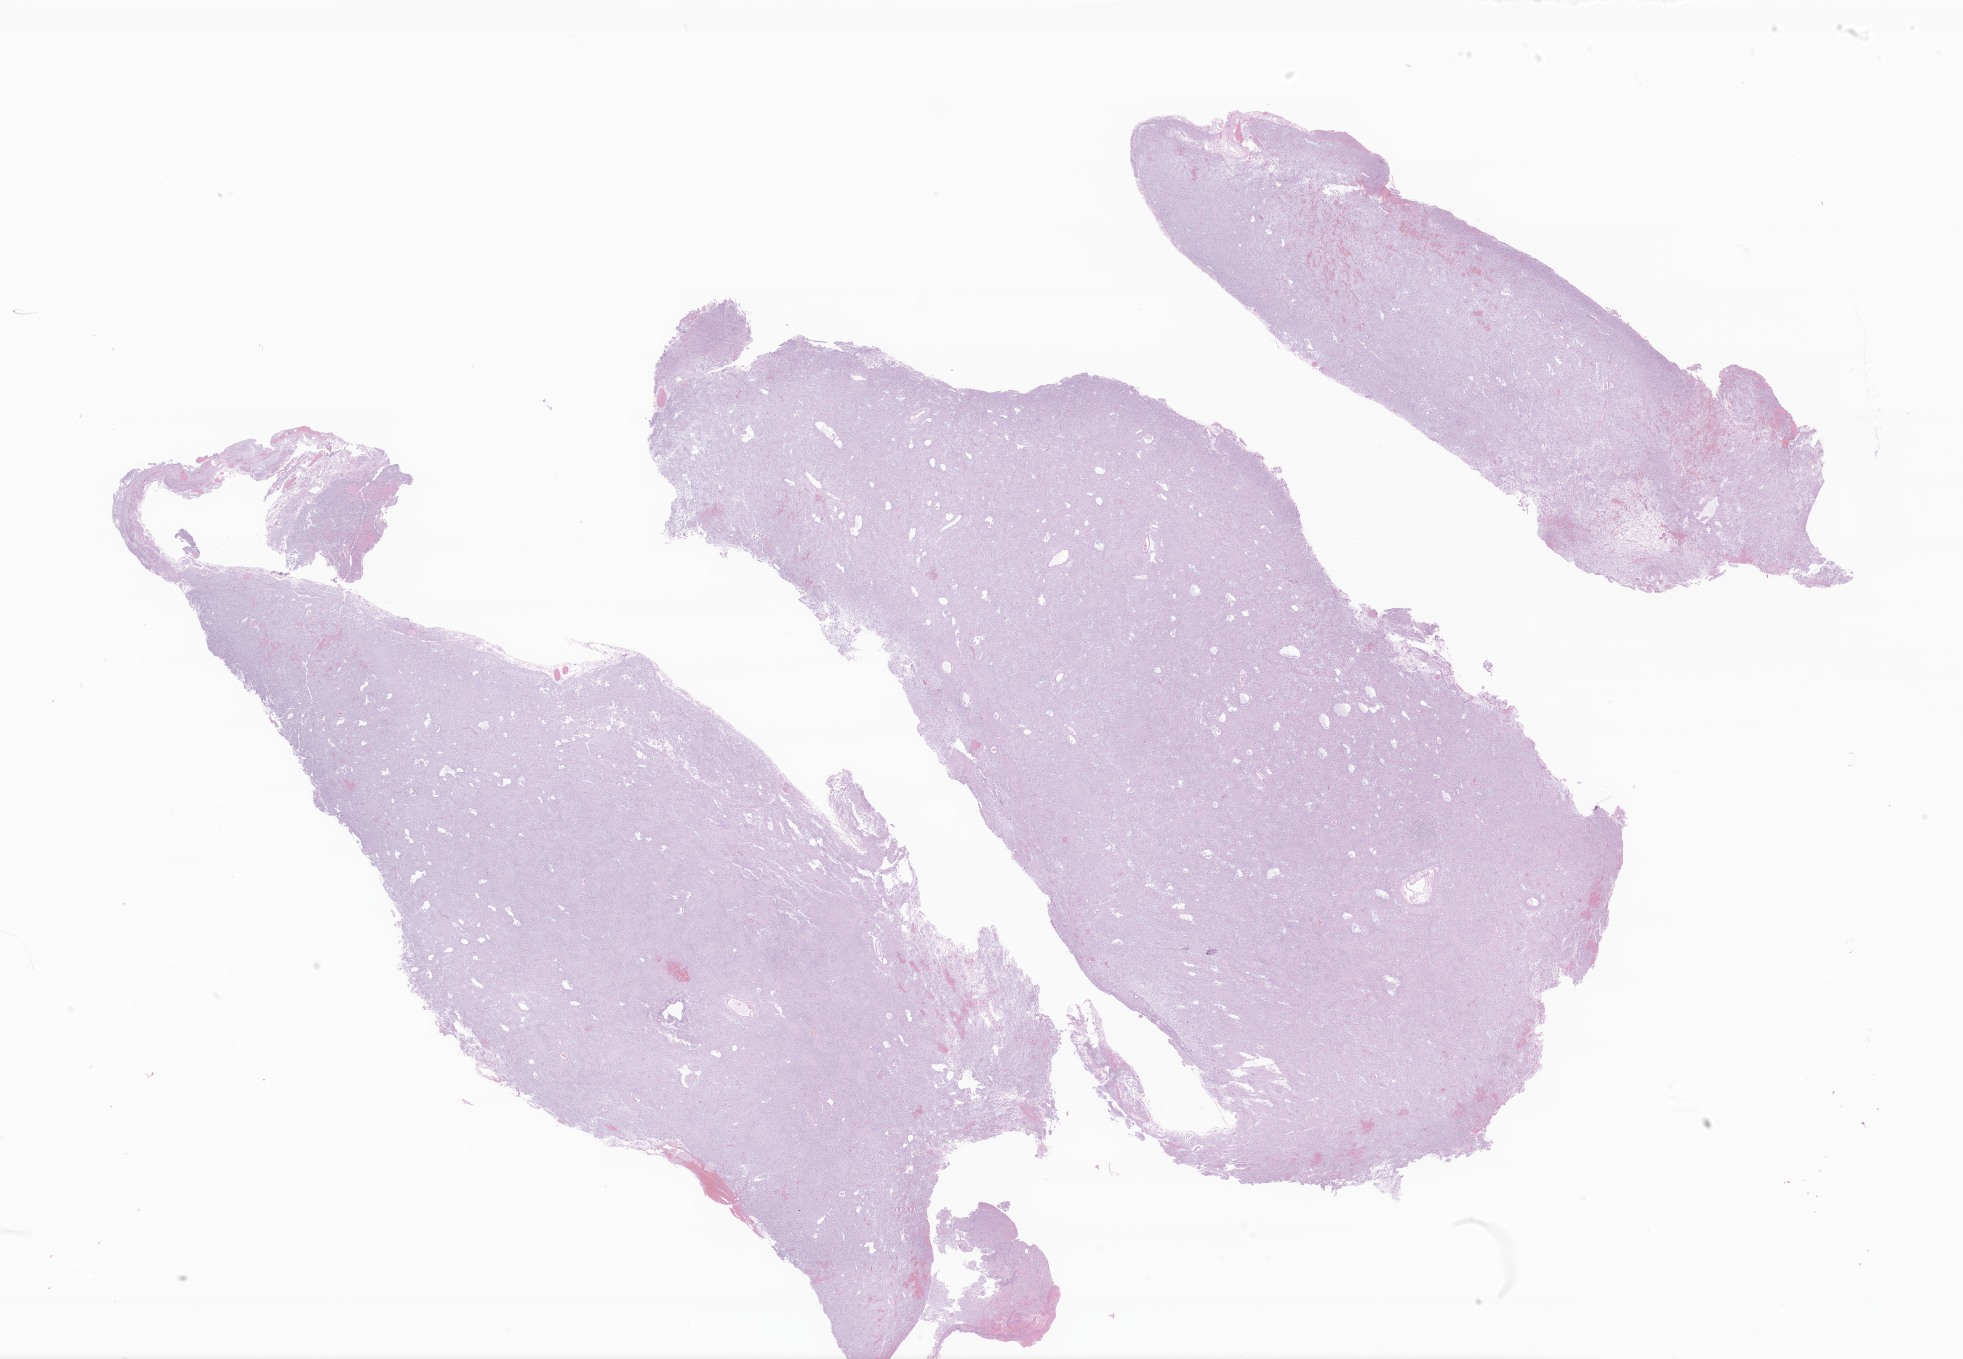
Digitized haematoxylin and eosin-stained section of tumor tissue from the brain — whole scanned area (about 33.1 x 22.9 mm) shown as a low-resolution overview, formalin-fixed, paraffin-embedded (FFPE) tissue. Patient: male, age 100 months (8 years 4 months).
Recorded diagnosis: Pilocytic astrocytoma.